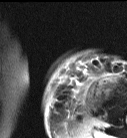
MRI of an extremity soft-tissue mass, one axial slice. Slice 15 of 87 in the series (ordered by position). T2-weighted fat-saturated. MR volume resampled by the dataset authors to the PET/CT grid (not the native acquisition matrix). 3.27 mm slice thickness. 127 × 138 image matrix, field of view 124 × 135 mm. Female patient. From the clinical record (not read from this slice): histological type: pleiomorphic leiomyosarcoma; grade: high; site of the primary tumour: left biceps.
Annotated regions visible in this slice (expert contour drawn on MRI and transferred to this co-registered scan by the dataset authors):
- gross tumour volume including surrounding oedema: box from (x=93, y=77) to (x=114, y=99) px